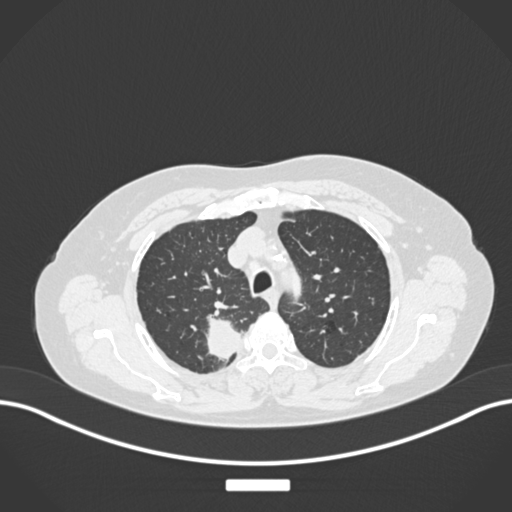
Chest CT, one axial slice. Reconstruction kernel B30f. 120 kVp. Lung window (W 1500 / L -600 HU). 1 mm slice thickness. 512 × 512 image matrix, field of view 400 × 400 mm. Patient: female, 62 years. Case-level facts recorded for this patient, not image findings: clinical TNM (as recorded): T1c N1 M0.
Outlined on this slice (rectangle marked by the reading radiologist):
- lung tumour (recorded histology: squamous cell carcinoma): bounding box <199,312,245,372> (left, top, right, bottom; pixels)